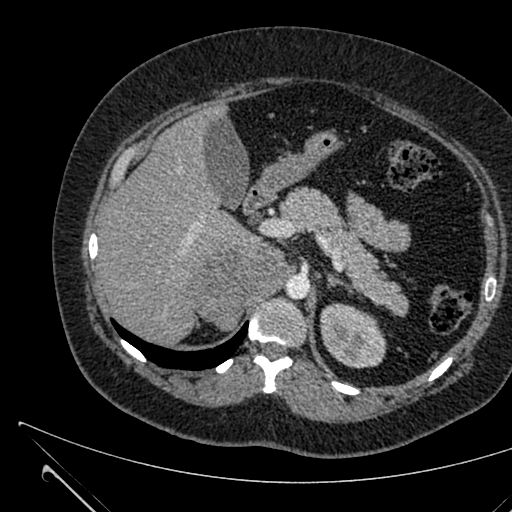
Contrast-enhanced abdominal CT, one axial slice; position 439 of 731 along the scan axis; soft-tissue window (W 400 / L 40 HU); 512 × 512 image matrix. Patient: female, 36 years. Case-level facts recorded for this patient, not image findings: diagnosis: adrenocortical carcinoma; tumour side: right adrenal; tumour size at pathology: 10 cm; Ki-67 index: 20 %; stage (as recorded): 4.
Structures marked on this image (semi-automatic segmentation, software-assisted and operator-edited):
- mass: box from (x=187, y=244) to (x=289, y=330) px